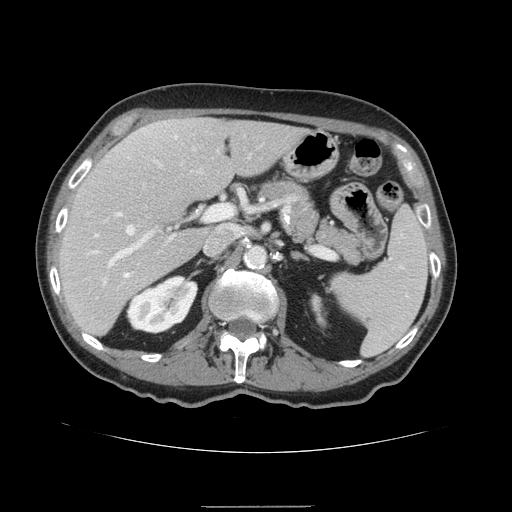
Contrast-enhanced abdominal CT, one axial slice; position 88 of 168 along the scan axis; 120 kVp; intravenous contrast given; soft-tissue window (W 400 / L 40 HU); 2.5 mm slice thickness; 512 × 512 image matrix. Male patient, age 74 years. From the clinical record (not read from this slice): diagnosis: colorectal cancer liver metastases, imaged before liver resection; multiple liver metastases: no; largest metastasis: 14.5 cm.
Annotated regions visible in this slice (expert manual segmentation):
- hepatic veins: box from (x=125, y=225) to (x=135, y=276) px
- liver: (x=59, y=118)–(x=309, y=336)
- planned liver remnant (the part of the liver to remain after resection): (x=59, y=120)–(x=309, y=336)
- portal vein (with intrahepatic branches): (x=87, y=206)–(x=231, y=269)